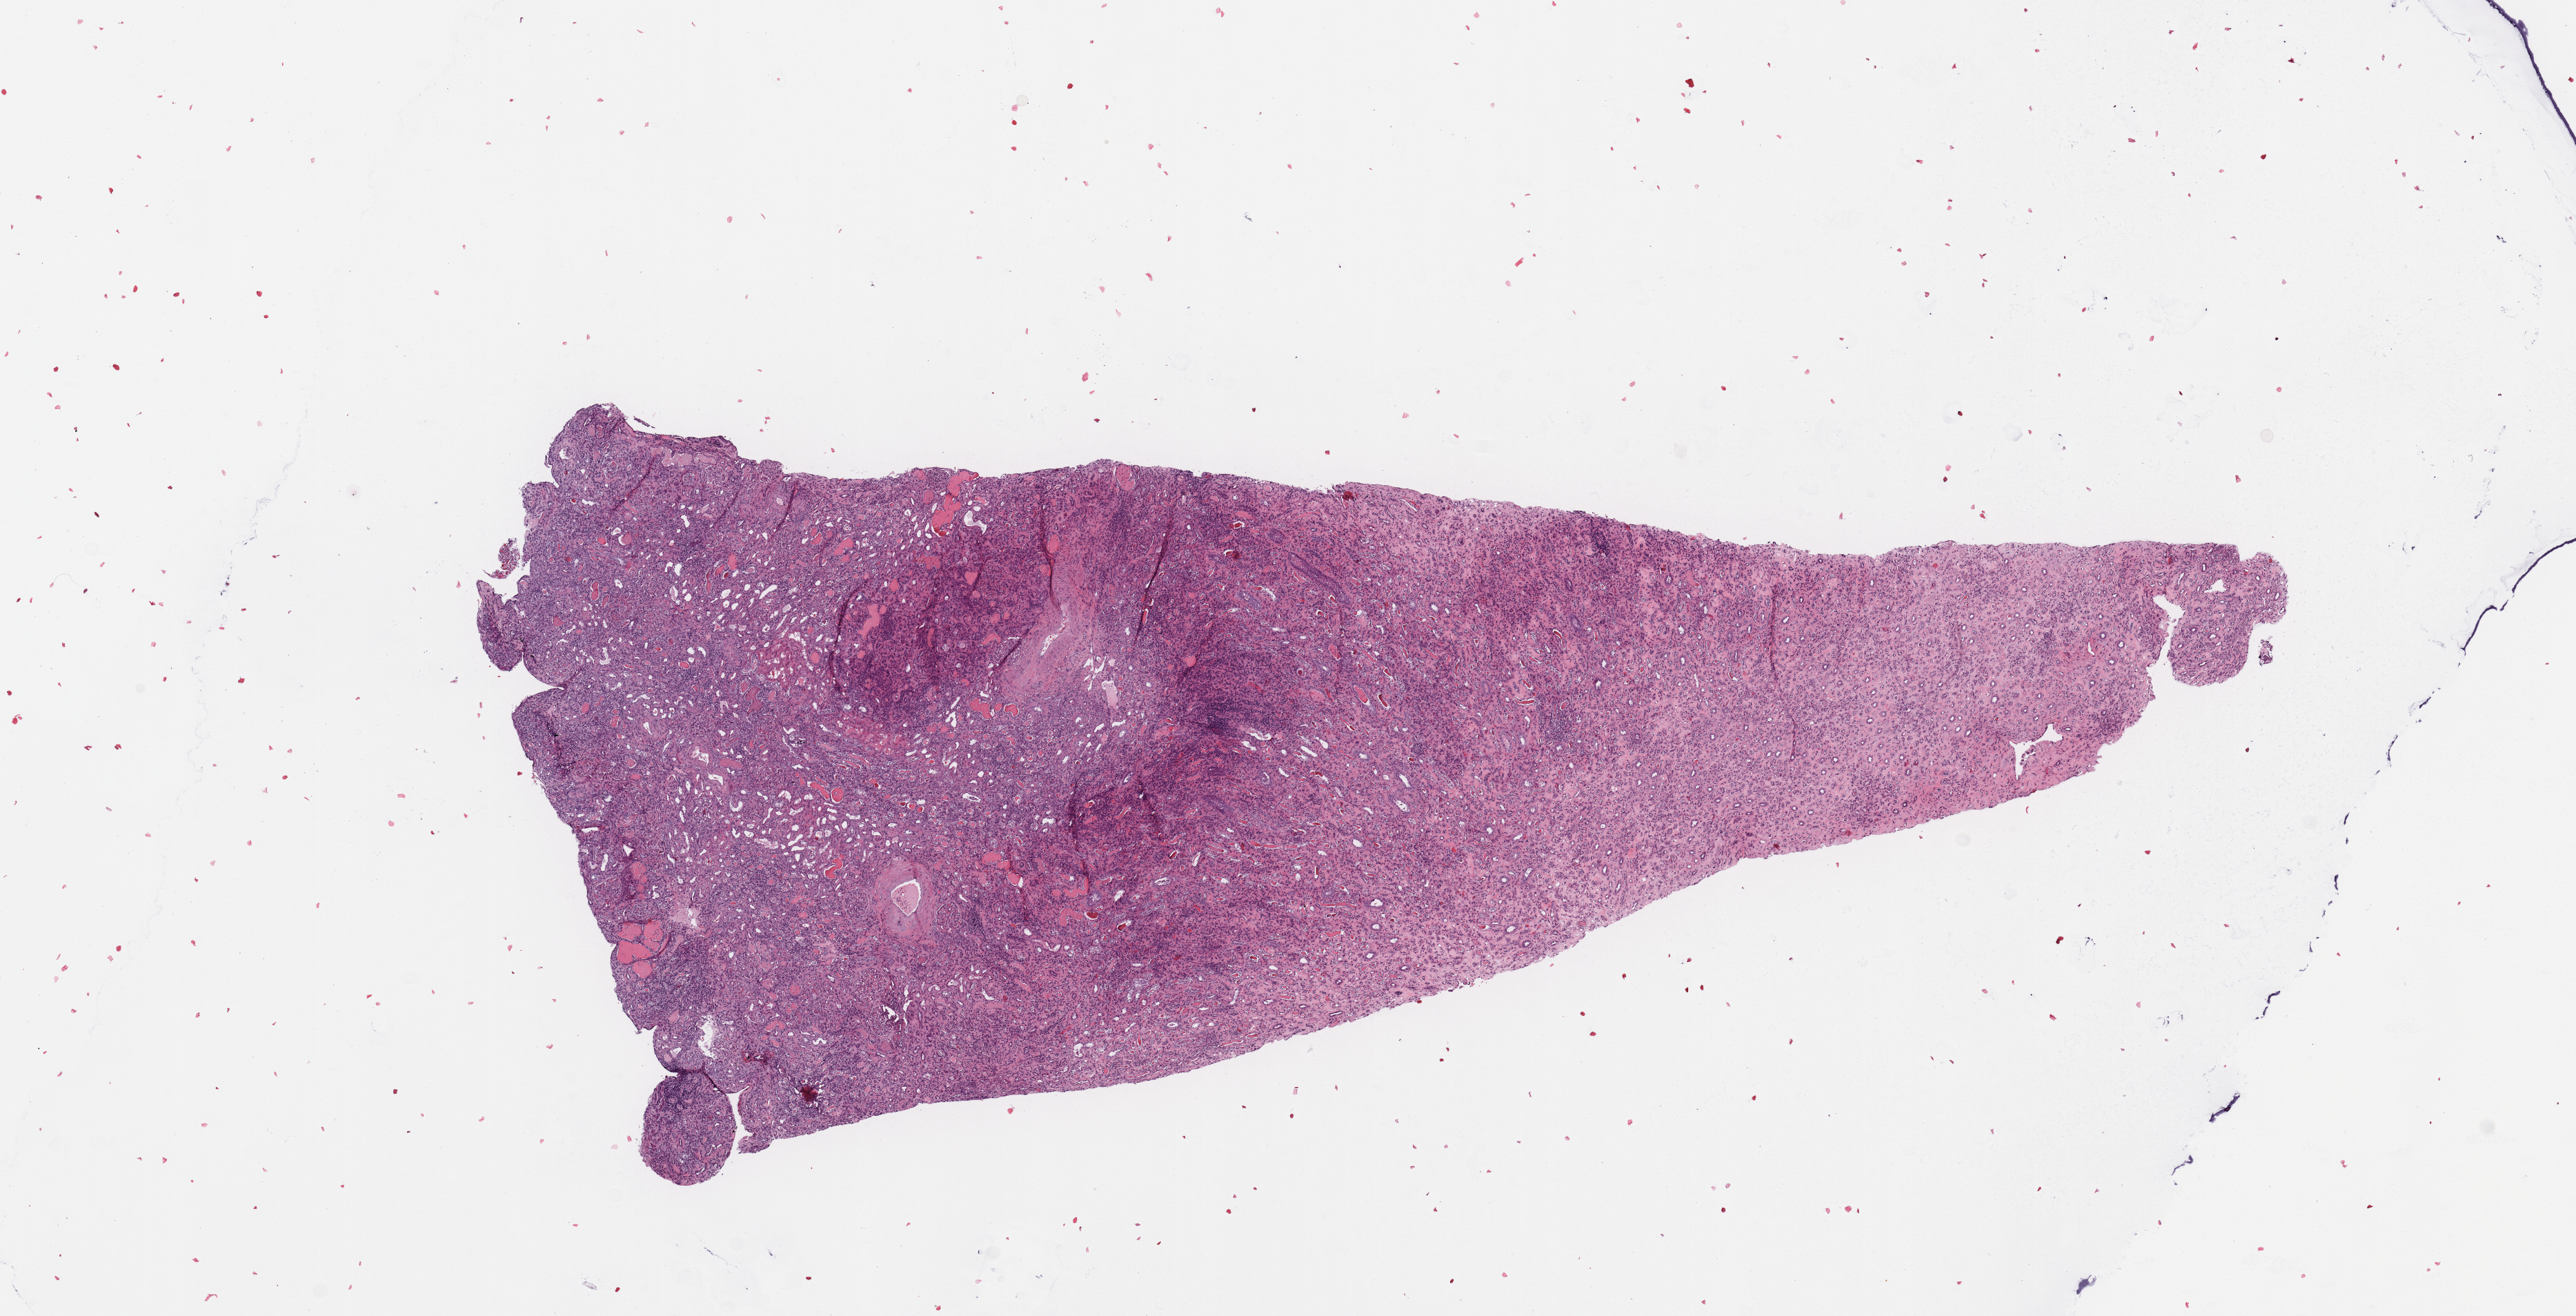
Whole-slide histology image, Hematoxylin and eosin (H&E) stained — shown as a low-resolution overview of the whole scanned area (about 14.8 x 7.5 mm, from a 20x scan); kidney, normal (non-tumour) tissue. Male, 47 y/o.
• this section: normal (non-tumour) tissue from the same patient
• patient diagnosis: Renal cell carcinoma, NOS